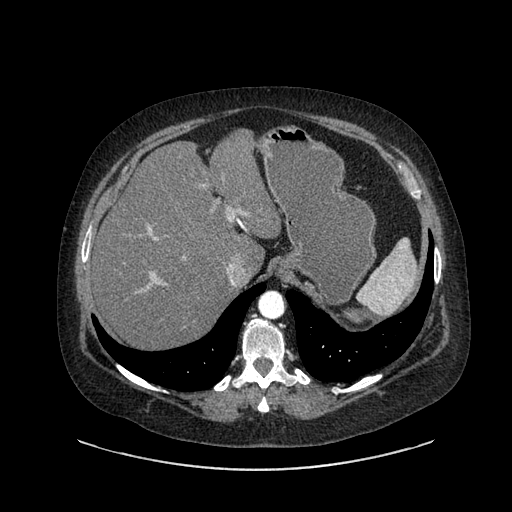
Contrast-enhanced abdominal CT, one axial slice; position 646 of 769 along the scan axis; 120 kVp; intravenous contrast given; soft-tissue window (W 400 / L 40 HU); 0.62 mm slice thickness; 512 × 512 image matrix, field of view 460 × 460 mm. Female patient, age 61 years. From the clinical record (not read from this slice): diagnosis: adrenocortical carcinoma; tumour side: left adrenal; tumour size at pathology: 13 cm; Ki-67 index: 79 %; stage (as recorded): 2.
Outlined on this slice (semi-automatically segmented with operator editing):
- mass: bounding box (x1, y1, x2, y2) in pixels: (338, 305, 367, 330)